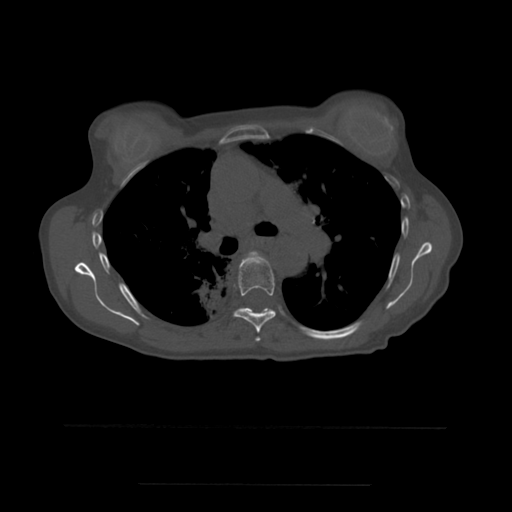
CT including the spine, one axial slice; bone window (W 1800 / L 400 HU); 512 × 512 image matrix, field of view 350 × 350 mm. Patient age 58 years. Case-level facts recorded for this patient, not image findings: primary cancer: lung.
Structures marked on this image (semi-automatically segmented with operator editing):
- T5 vertebra: bounding box [x1, y1, x2, y2] px = [247, 252, 261, 342]
- T6 vertebra: [234, 253, 276, 333]
- T7 vertebra: [268, 309, 271, 311]